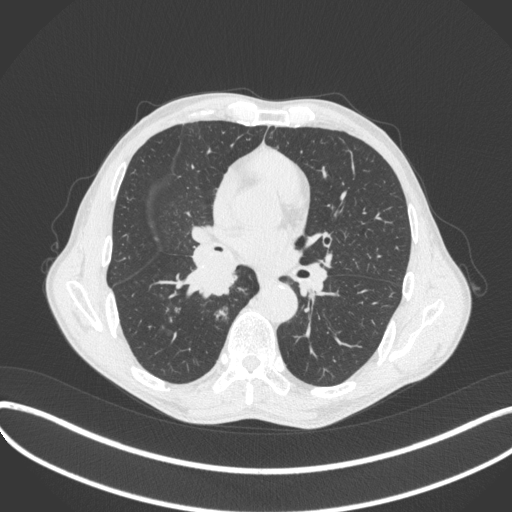
Chest CT, one axial slice; position 223 of 481 along the scan axis; reconstruction kernel B31f; lung window (W 1500 / L -600 HU); 1 mm slice thickness; 512 × 512 image matrix, field of view 400 × 400 mm. Male patient, age 65 years. Case-level facts recorded for this patient, not image findings: clinical TNM (as recorded): T2a N0 M0; histopathological grade: G2.
Structures marked on this image (bounding box drawn by a radiologist):
- lung tumour (recorded histology: squamous cell carcinoma): bounding box [x1, y1, x2, y2] px = [178, 239, 245, 300]